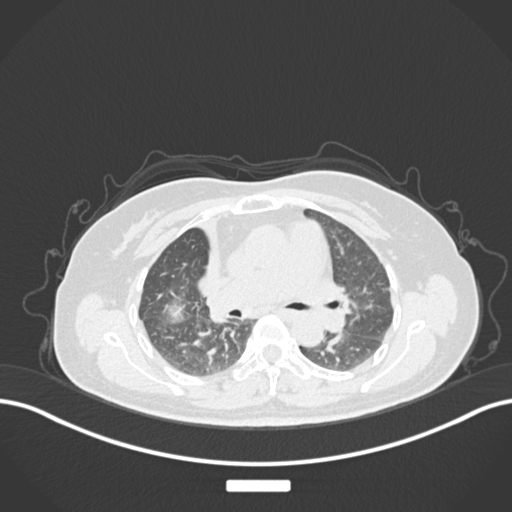
Chest CT, one axial slice; position 89 of 177 along the scan axis; 120 kVp; lung window (W 1500 / L -600 HU); 1 mm slice thickness; 512 × 512 image matrix, field of view 400 × 400 mm. Patient: female, 60 years. Case-level facts recorded for this patient, not image findings: clinical TNM (as recorded): T3 N1 M1.
Outlined on this slice (bounding box drawn by a radiologist):
- lung tumour (recorded histology: adenocarcinoma): bounding box [x1, y1, x2, y2] px = [151, 292, 197, 332]